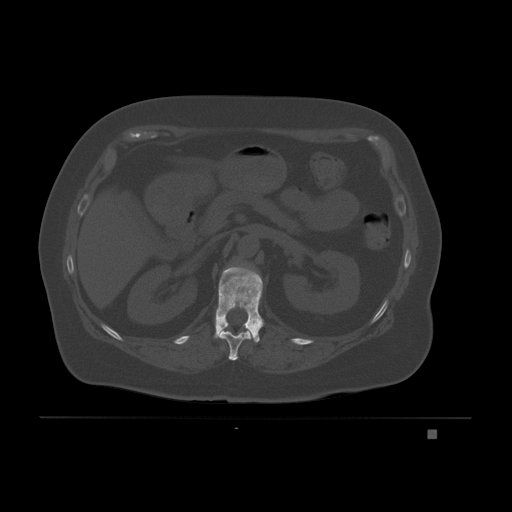
CT including the spine, one axial slice; position 82 of 221 along the scan axis; bone window (W 1800 / L 400 HU); 3 mm slice thickness; 512 × 512 image matrix, field of view 474 × 474 mm. Patient: female, 63 years. Case-level facts recorded for this patient, not image findings: primary cancer: breast.
Outlined on this slice (semi-automatic segmentation, software-assisted and operator-edited):
- T11 vertebra: bounding box <214,329,252,361> (left, top, right, bottom; pixels)
- T12 vertebra: <214,266,264,343>